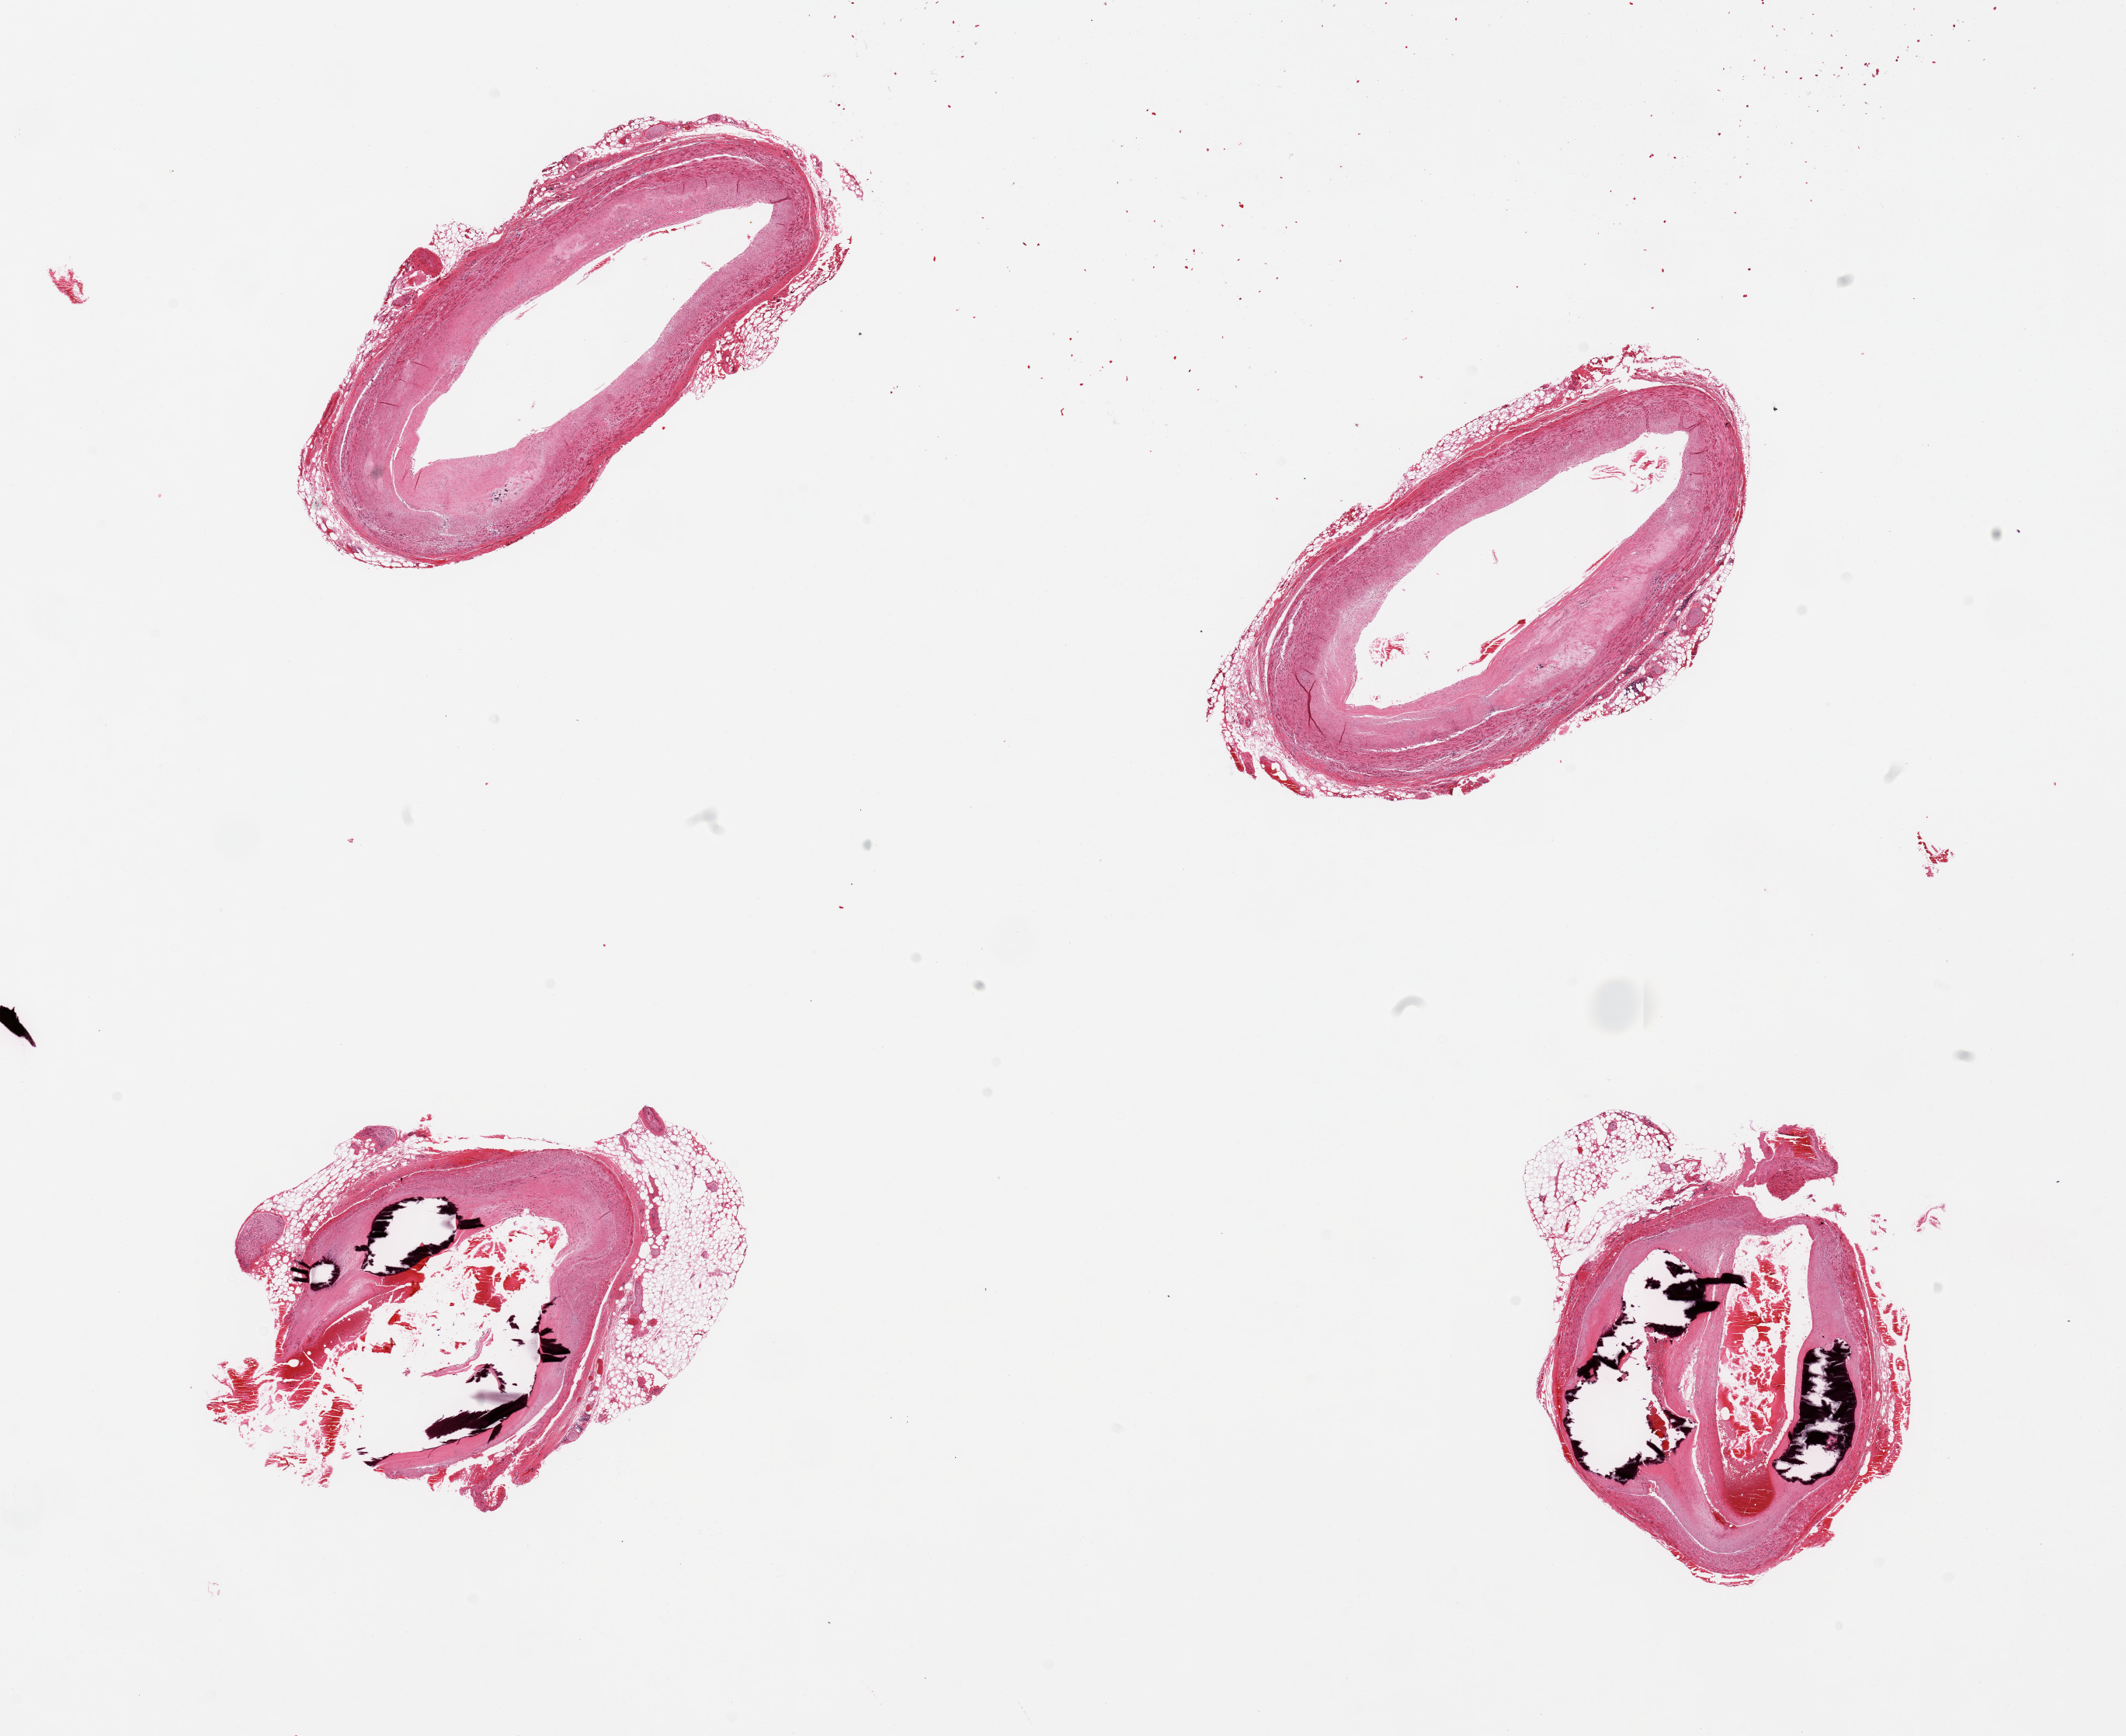
Whole-slide image, haematoxylin and eosin stain, brightfield, whole scanned area (about 21.7 x 17.7 mm, acquisition: 20x scan) shown as a low-resolution overview, PAXgene-fixed, paraffin-embedded tissue, section of coronary artery (target tissue), tissue donor sample.
Reviewer comment on this tissue sample: 4 pieces, 2 with ~60-70% occlusive atherosis, focally calcified.